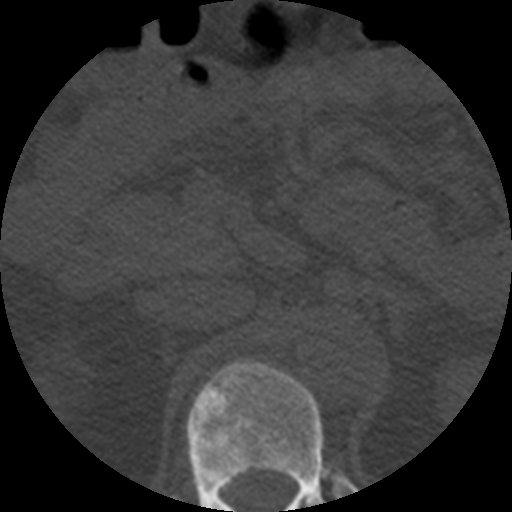
CT including the spine, one axial slice; reconstruction kernel STANDARD; 120 kVp; bone window (W 1800 / L 400 HU); 1.25 mm slice thickness; 512 × 512 image matrix. Patient age 57 years. From the clinical record (not read from this slice): primary cancer: prostate.
Structures marked on this image (semi-automatic segmentation, software-assisted and operator-edited):
- T12 vertebra: bounding box (x1, y1, x2, y2) in pixels: (186, 361, 352, 512)